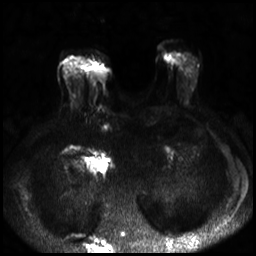
Breast MRI, one axial slice; position 8 of 30 along the scan axis; diffusion-weighted series; image 2 of 4 stored at this slice position (different b-values; order by instance number); 3 T; 4 mm slice thickness; 256 × 256 image matrix, field of view 320 × 320 mm. Female patient.
Structures marked on this image (manually delineated by an expert):
- tumour on diffusion-weighted imaging: box from (x=93, y=66) to (x=106, y=78) px